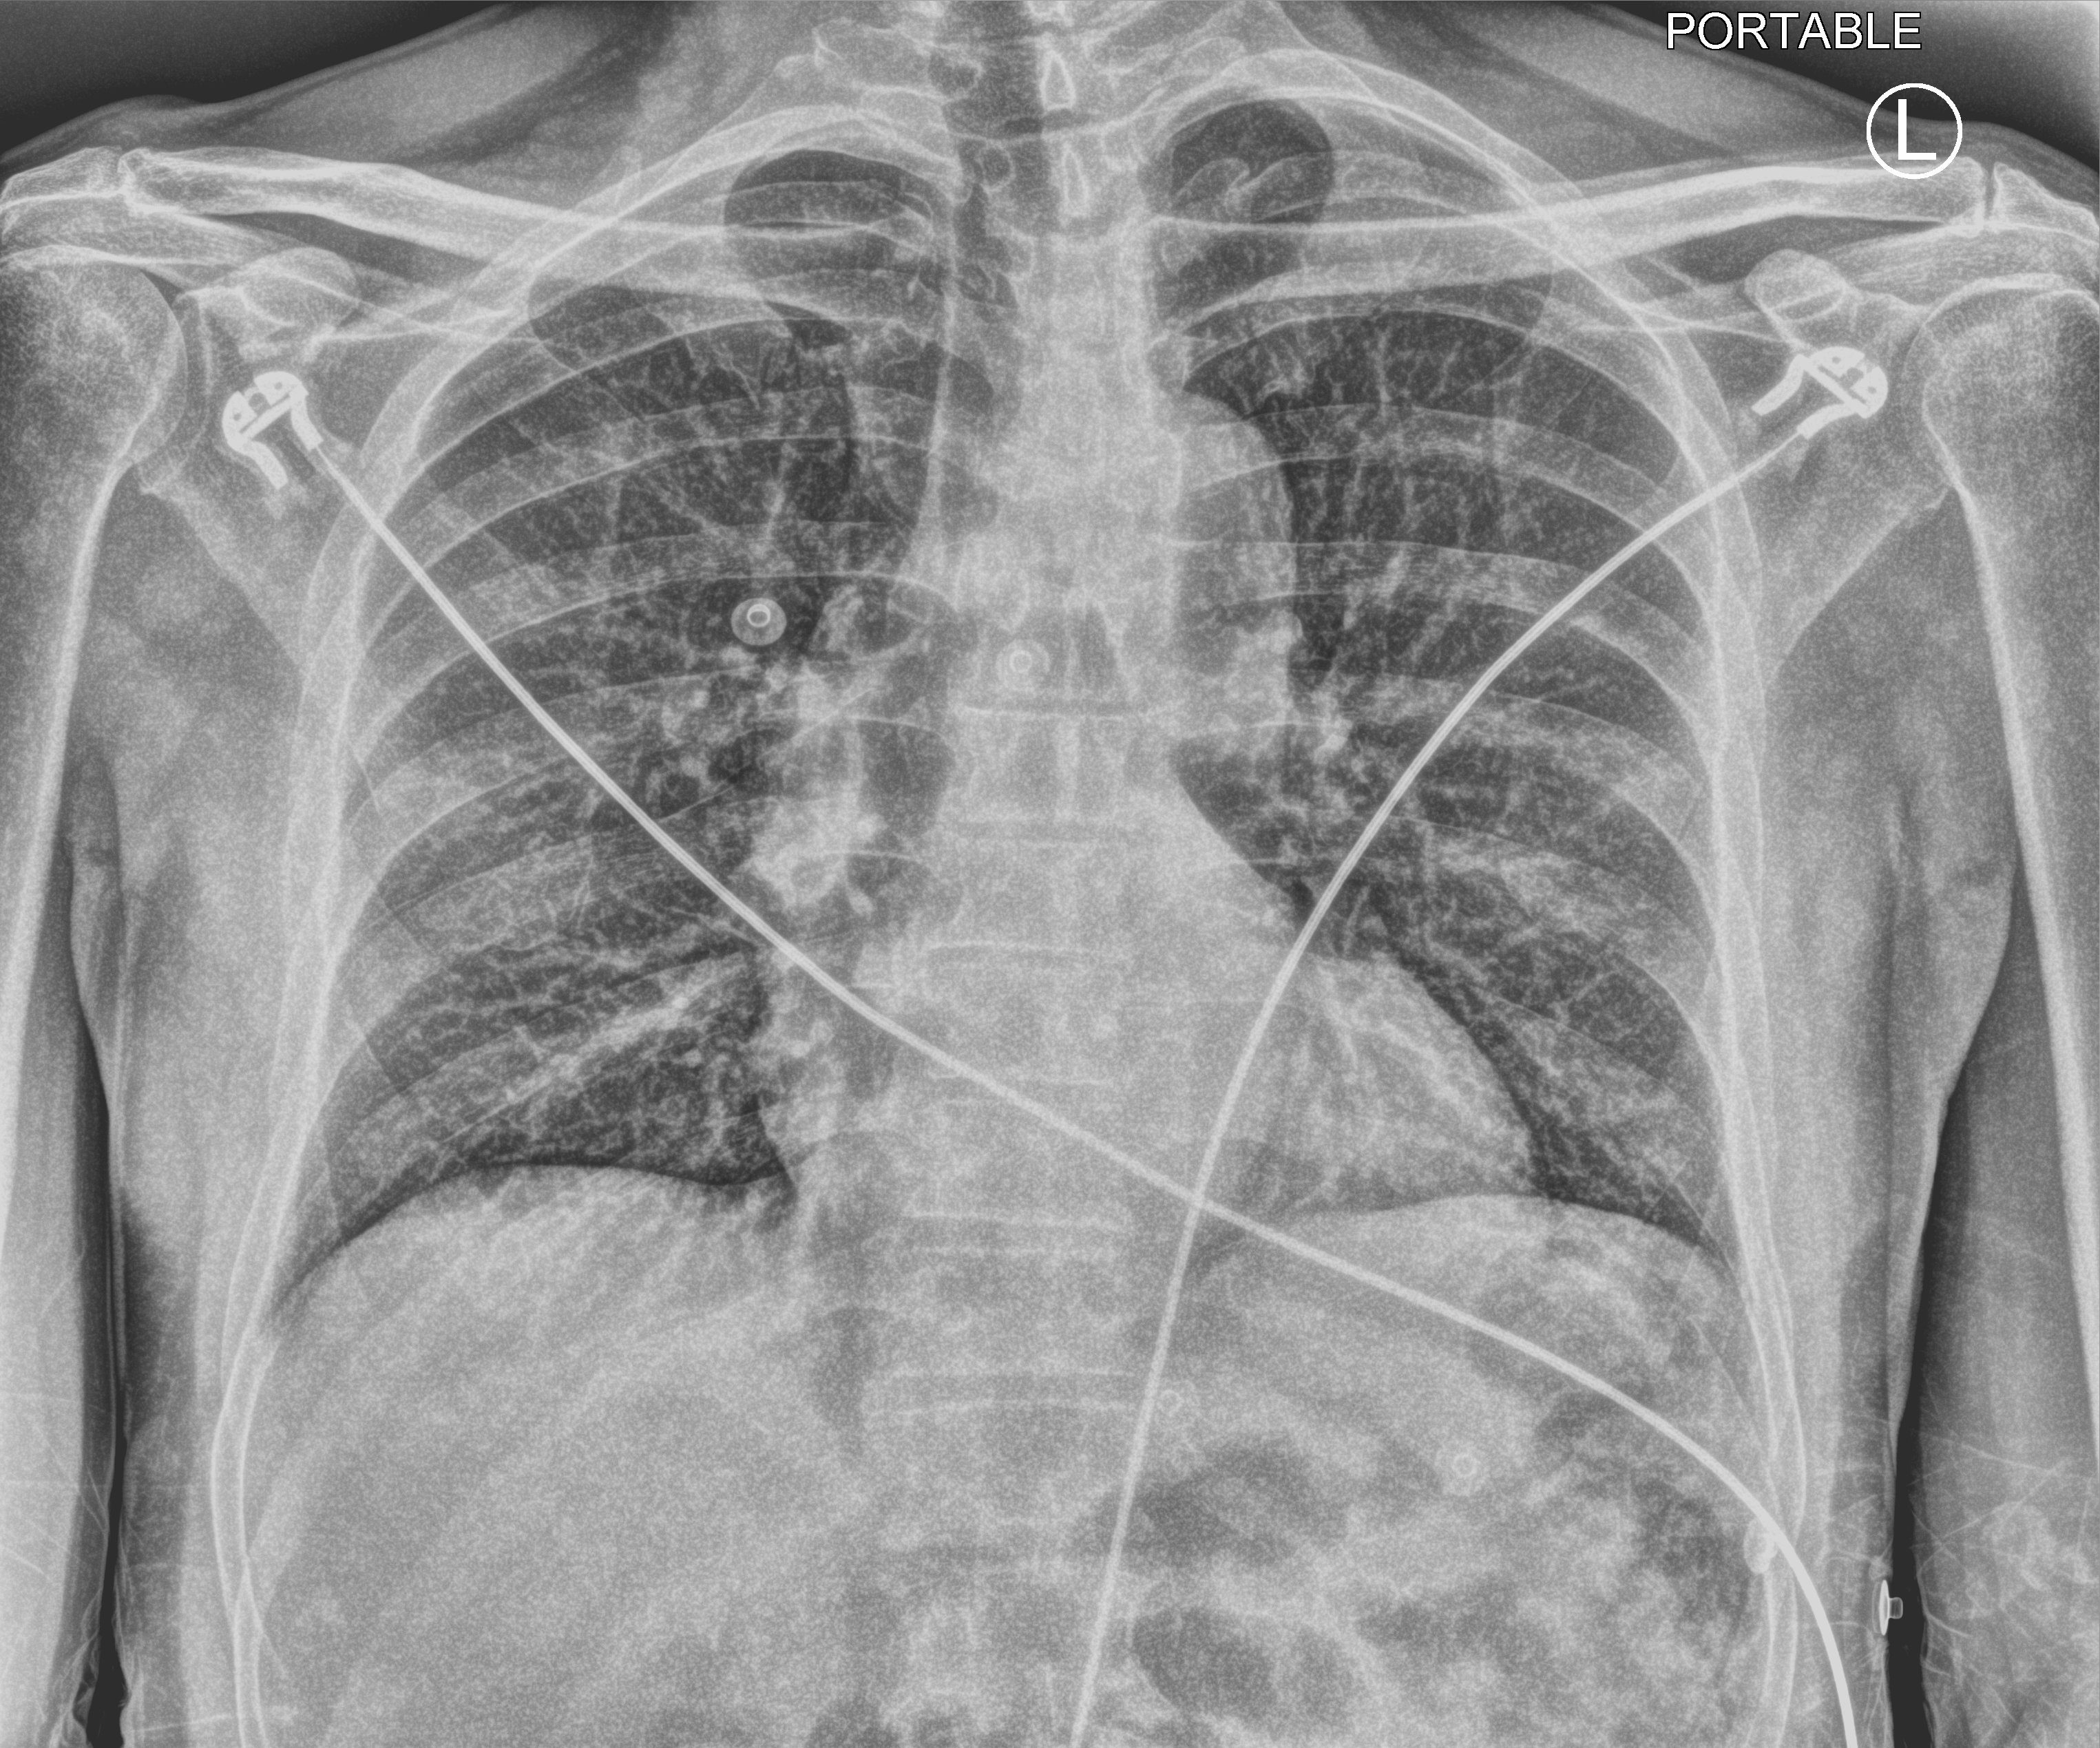
Chest X-ray (portable); anteroposterior (AP) projection. Patient hospitalised with COVID-19; male, aged 60–74 years.
Admission-level facts for this patient (not findings on this image; timing relative to this image not recorded): smoking status (admission record): never; admitted to intensive care during this hospital stay: no.